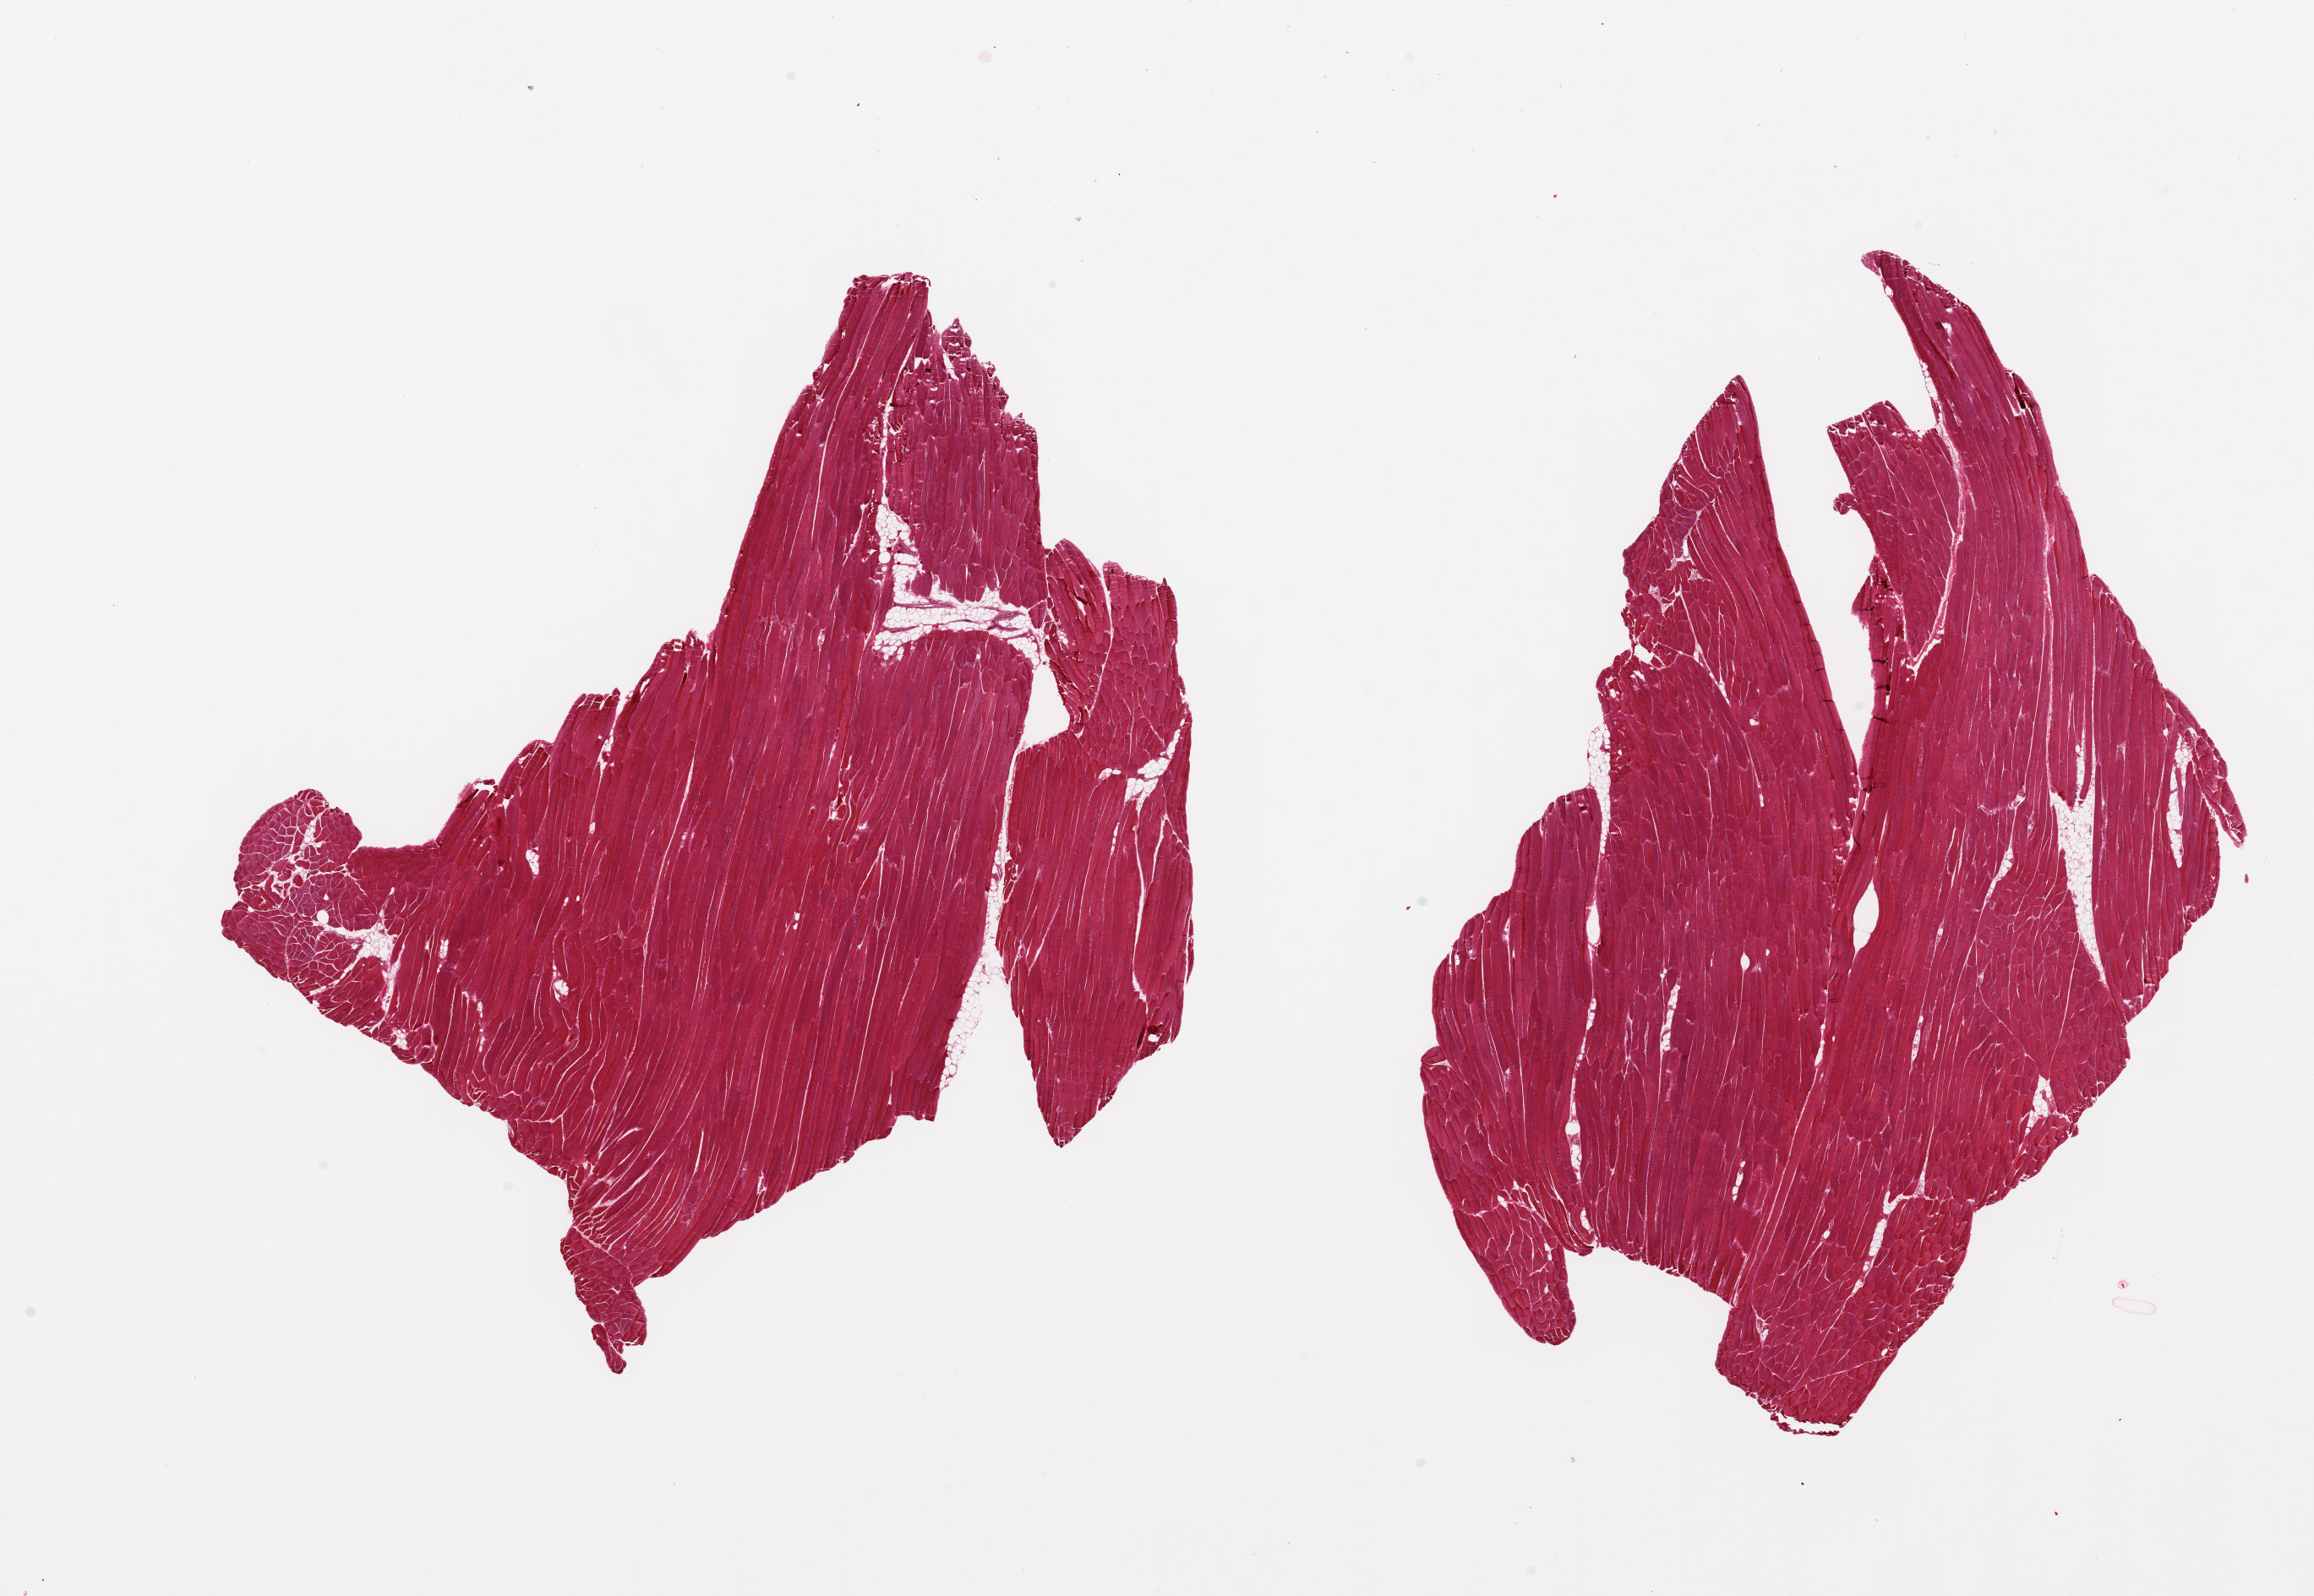
Digitized hematoxylin and eosin (H&E)-stained section, low-resolution overview of the scanned area, about 21.7 x 14.9 mm (from a 20x scan). PAXgene-fixed paraffin-embedded (PFPE) section. Section of skeletal muscle (target tissue). Tissue donor sample. Donor sex: male.
* reviewer comment on this tissue sample: 2 pieces; <5% internal fat